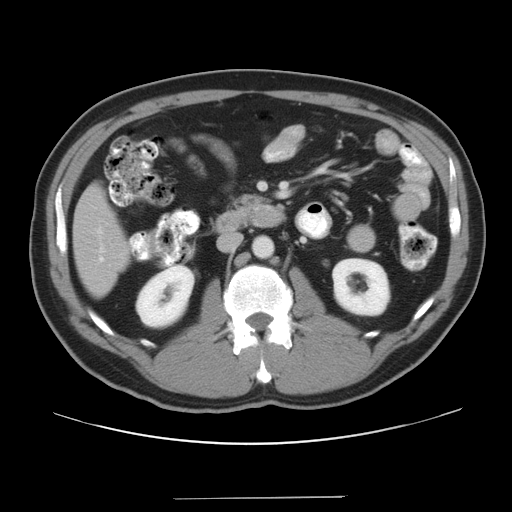
Contrast-enhanced abdominal CT, one axial slice; 120 kVp; intravenous contrast given; soft-tissue window (W 400 / L 40 HU); 512 × 512 image matrix, field of view 400 × 400 mm. Male patient, age 46 years. From the clinical record (not read from this slice): diagnosis: colorectal cancer liver metastases, imaged before liver resection; multiple liver metastases: yes; largest metastasis: 1 cm; disease in both lobes: no.
Outlined on this slice (manually delineated by an expert):
- hepatic veins: box from (x=99, y=249) to (x=104, y=261) px
- liver: (x=74, y=189)–(x=128, y=296)
- planned liver remnant (the part of the liver to remain after resection): (x=74, y=189)–(x=128, y=296)